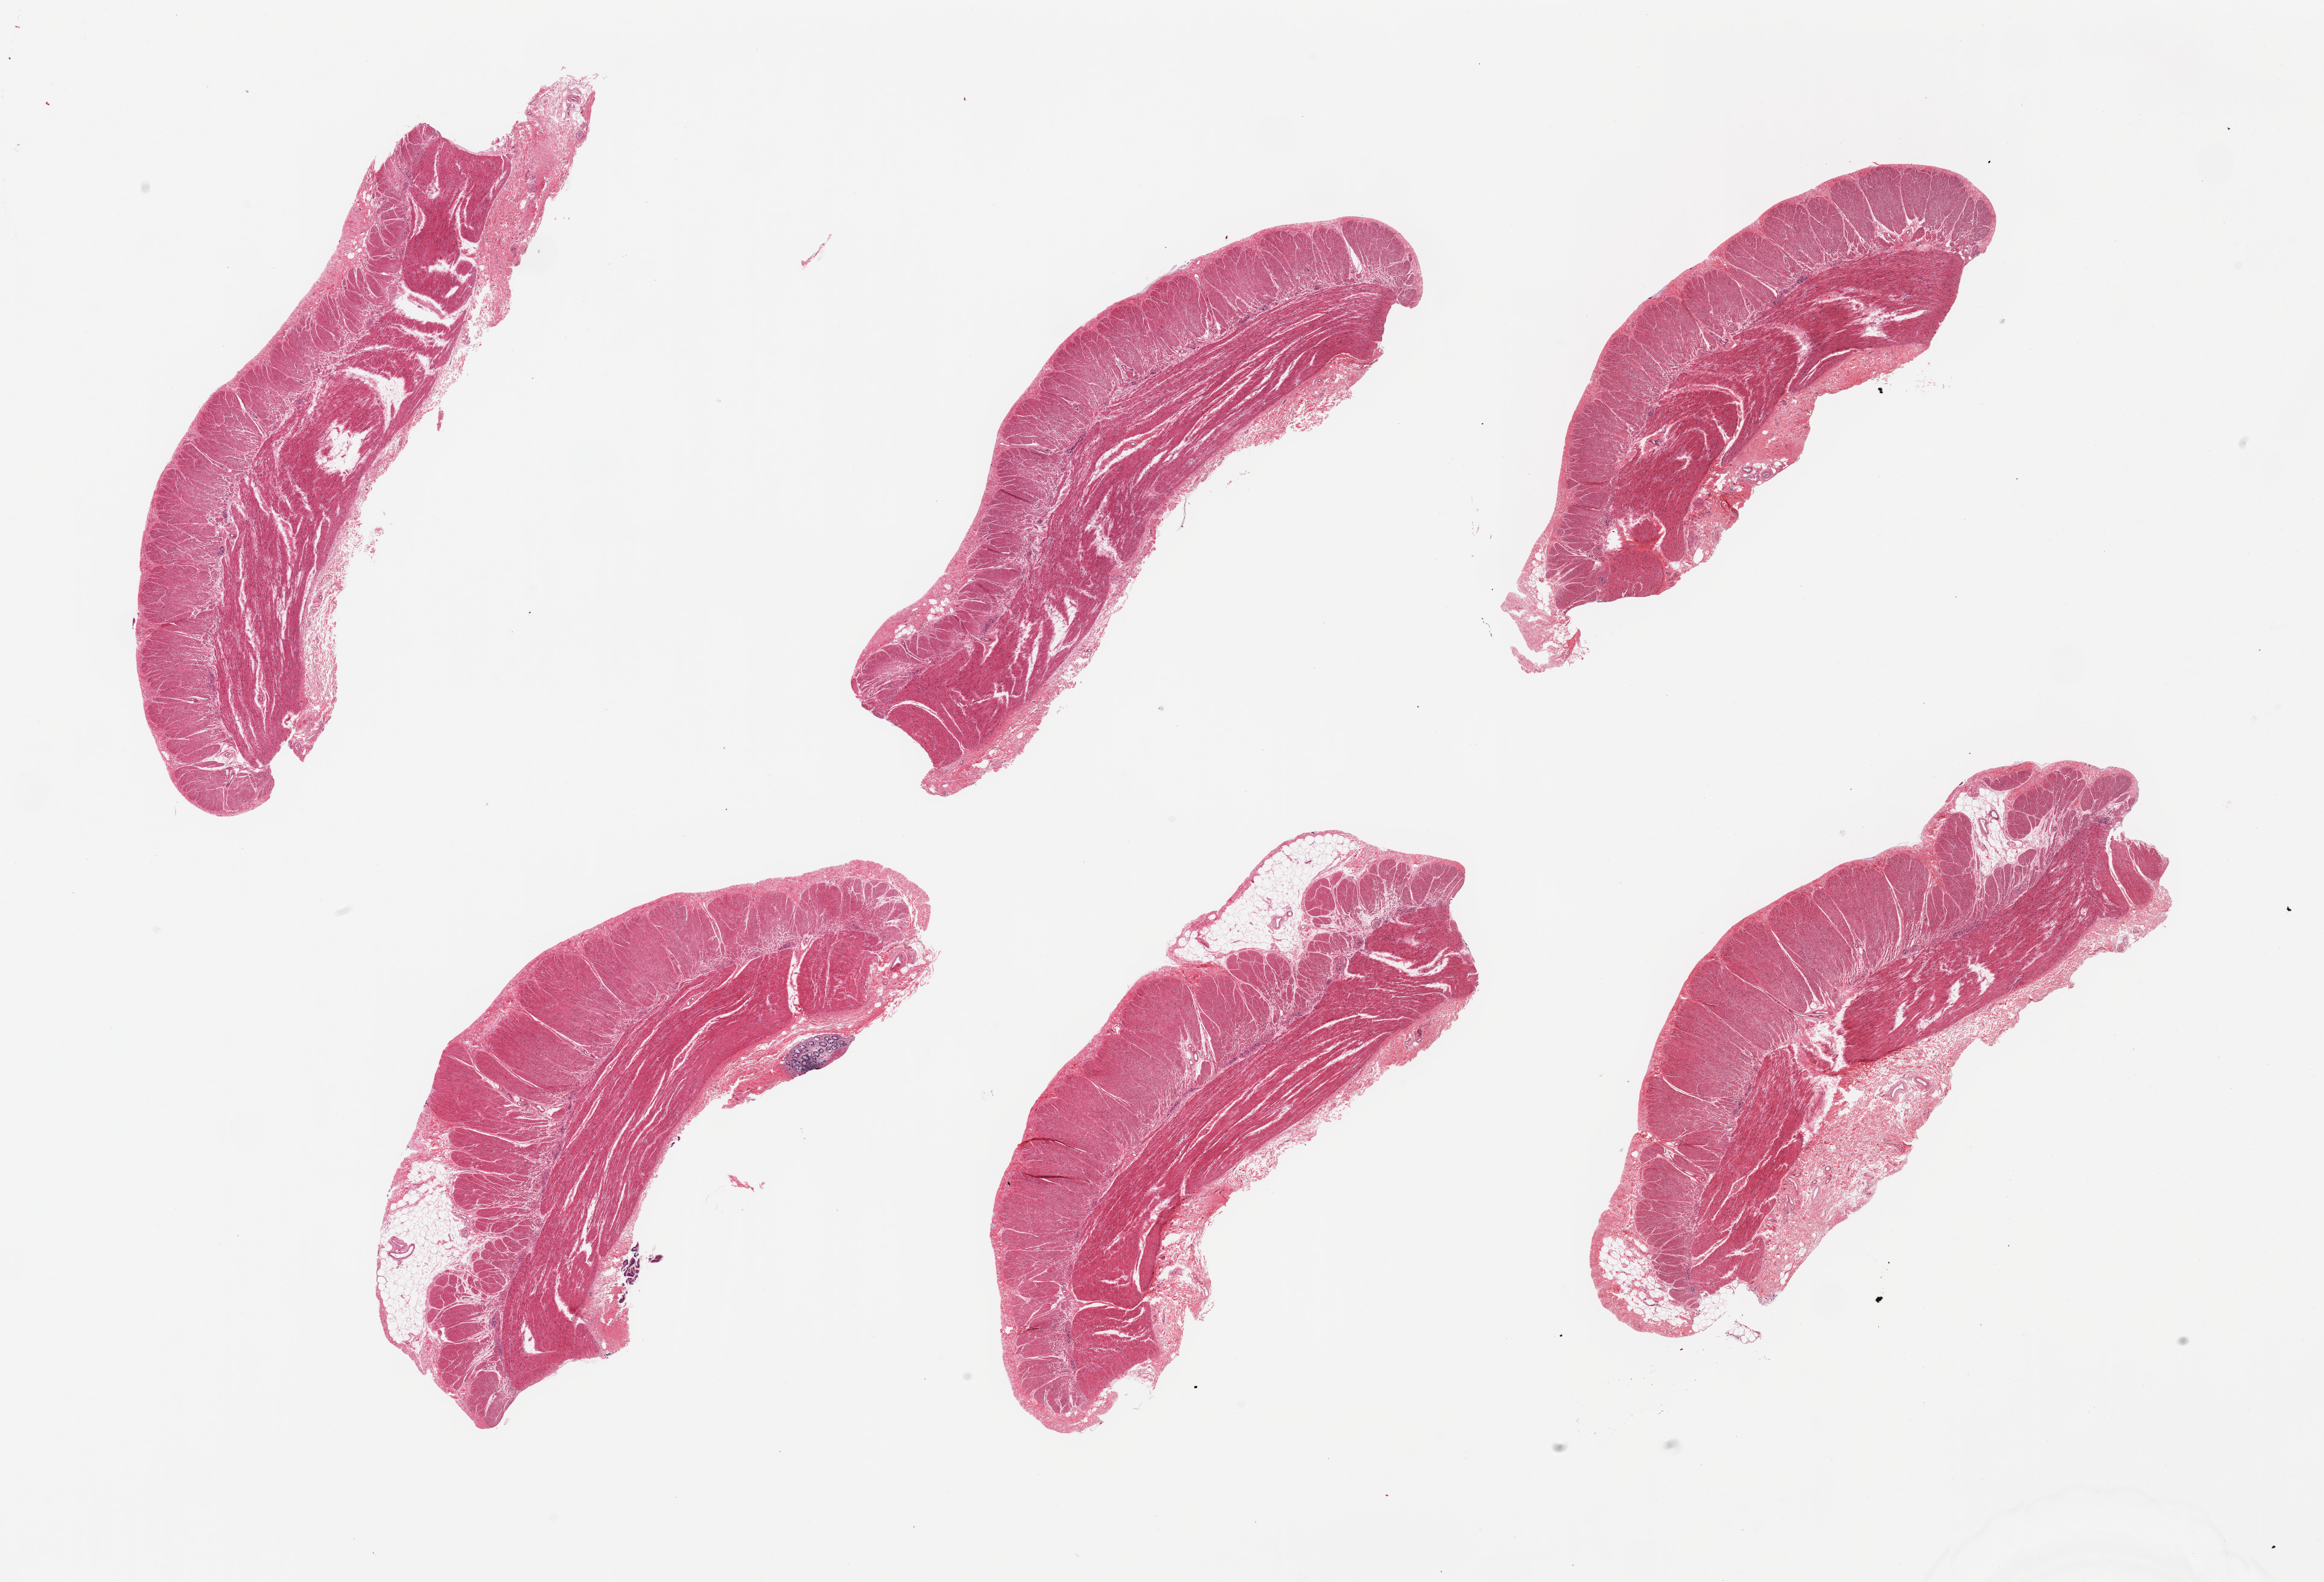
Digitized hematoxylin and eosin (H&E)-stained section — a low-resolution overview of the entire scanned area, about 30.5 x 20.8 mm (slide scanned at 20x); PAXgene-fixed, paraffin-embedded tissue; target tissue: sigmoid colon; tissue donor sample. Donor sex: female.
- review note (as recorded): 6 pieces, all muscularis, trace adherent serosa